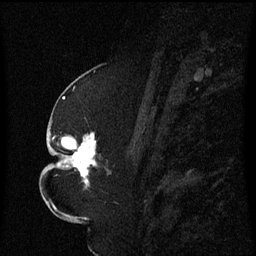
Breast MRI (dynamic contrast-enhanced), one sagittal slice; slice 32 of 60 in the series (ordered by position); dynamic contrast-enhanced series, image 2 of 3 at this slice position (ordered by acquisition); 1.5 T; TE 4.2 ms, TR 8.4 ms; 256 × 256 image matrix, field of view 200 × 200 mm. Patient: female, 52 years. Case-level facts recorded for this patient, not image findings: setting: breast cancer imaged before/during neoadjuvant chemotherapy; receptor status: HR-positive, HER2-negative.
Outlined on this slice (semi-automatically segmented with operator editing):
- analysis volume of interest (the breast-tissue region the enhancement analysis was run in; not a lesion): bounding box <49,124,111,191> (left, top, right, bottom; pixels)
- tumour enhancement mask (voxels above the 70 % enhancement threshold inside the analysis volume of interest): <57,132,97,187>